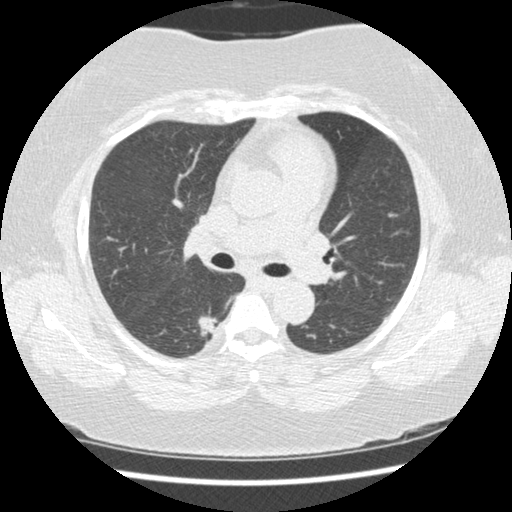
Chest CT (low-dose screening protocol), one axial image; second screening round (one year after baseline); lung window (W 1500 / L -600 HU); 1.25 mm slice thickness; slice 72 of 210 in the series. Female participant, aged 58 years at enrolment. Current smoker at enrolment.
Lesion marked by an expert reader, bounding box (x1, y1, x2, y2) in pixels: (189, 309, 228, 350). The exam's reader record, not a measurement of the box and not confirmed to be the same lesion: non-calcified nodule or mass ≥4 mm, right lower lobe, 15 × 15 mm, spiculated (stellate) margins, soft tissue attenuation, pre-existing on the prior screen: yes; interval growth: yes. Official screen result: positive, change unspecified: nodule(s) >= 4 mm or enlarging nodule(s), mass(es), or other non-specific abnormalities suspicious for lung cancer. Later outcome: lung cancer diagnosed 21 days after this screen — adenocarcinoma, NOS, right lower lobe, stage IB (AJCC 6th edition), 15 mm at pathology.